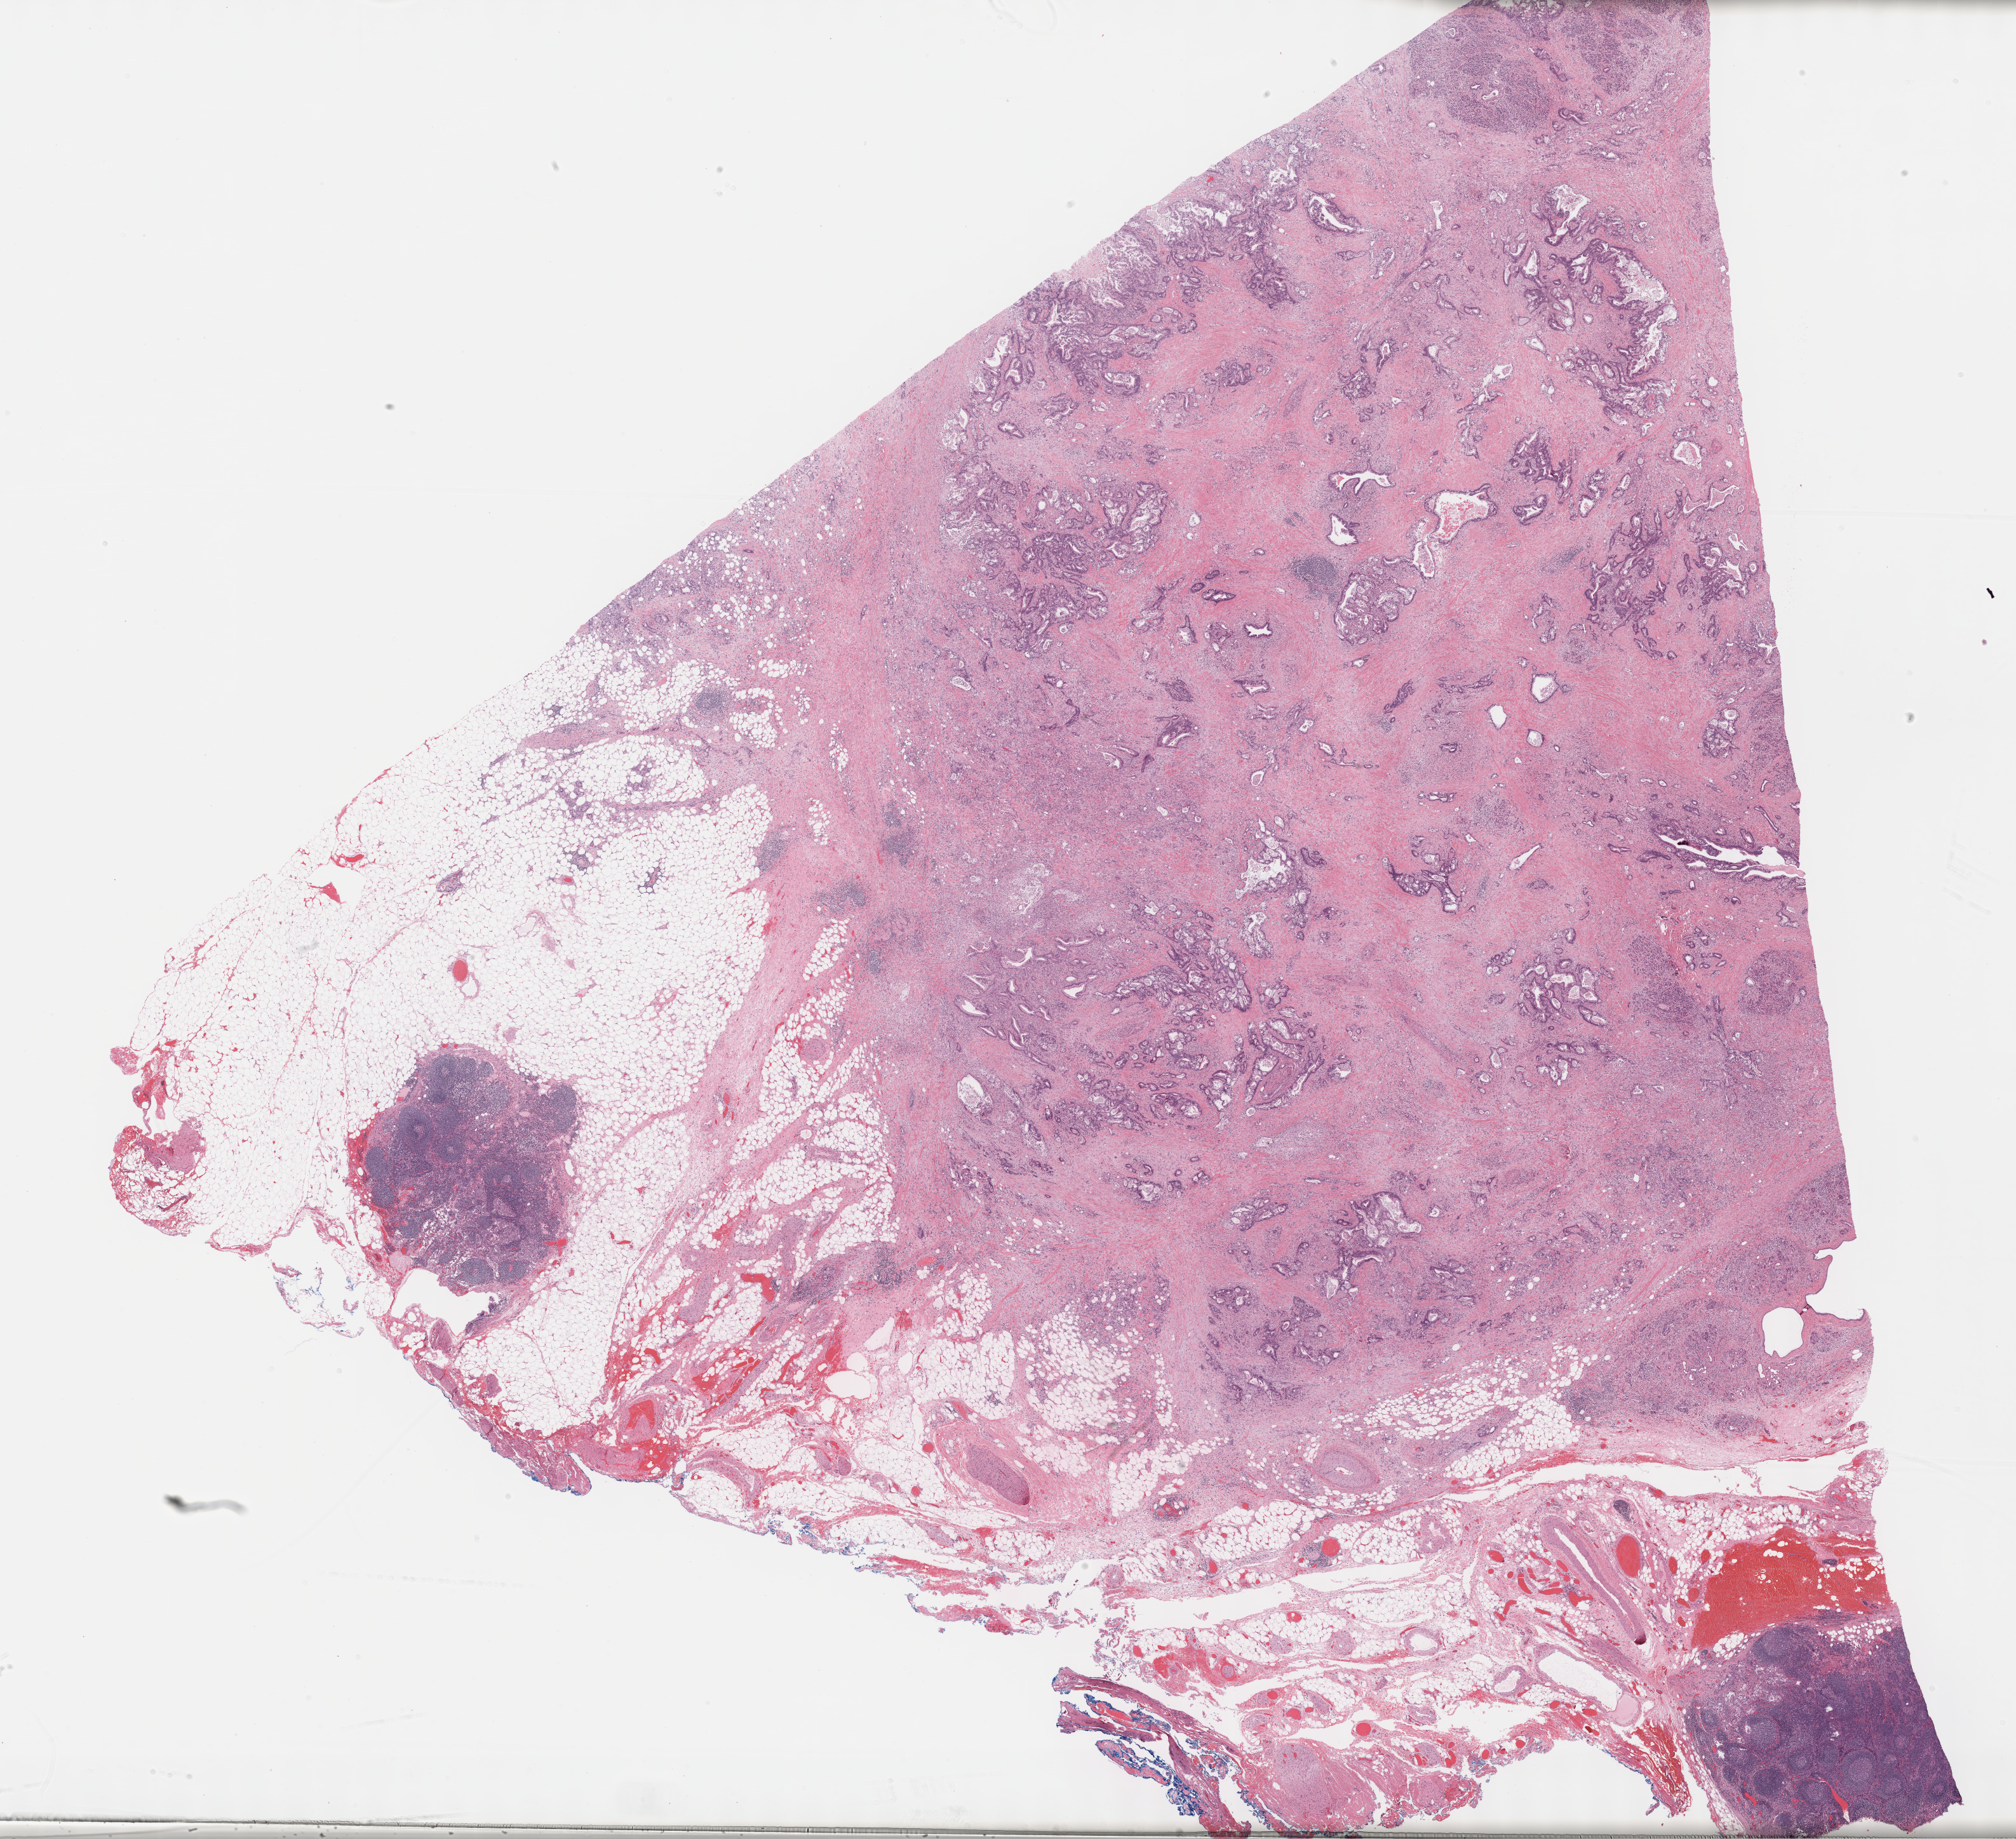
Whole-slide histology image, Hematoxylin and eosin (H&E) stained — a low-resolution overview of the entire scanned area, about 25.7 x 23.4 mm, formalin-fixed paraffin-embedded (FFPE) diagnostic section, pancreas, primary tumour sample. Patient: male, age at initial diagnosis 59 years. Histologic grade: G2 (moderately differentiated).
AJCC pathologic stage: IIB (7th edition). TNM: T3 N1 M0. Histologic diagnosis: Infiltrating duct carcinoma, NOS (head of pancreas). Lymph nodes positive (case pathology): 3 of 24 examined.